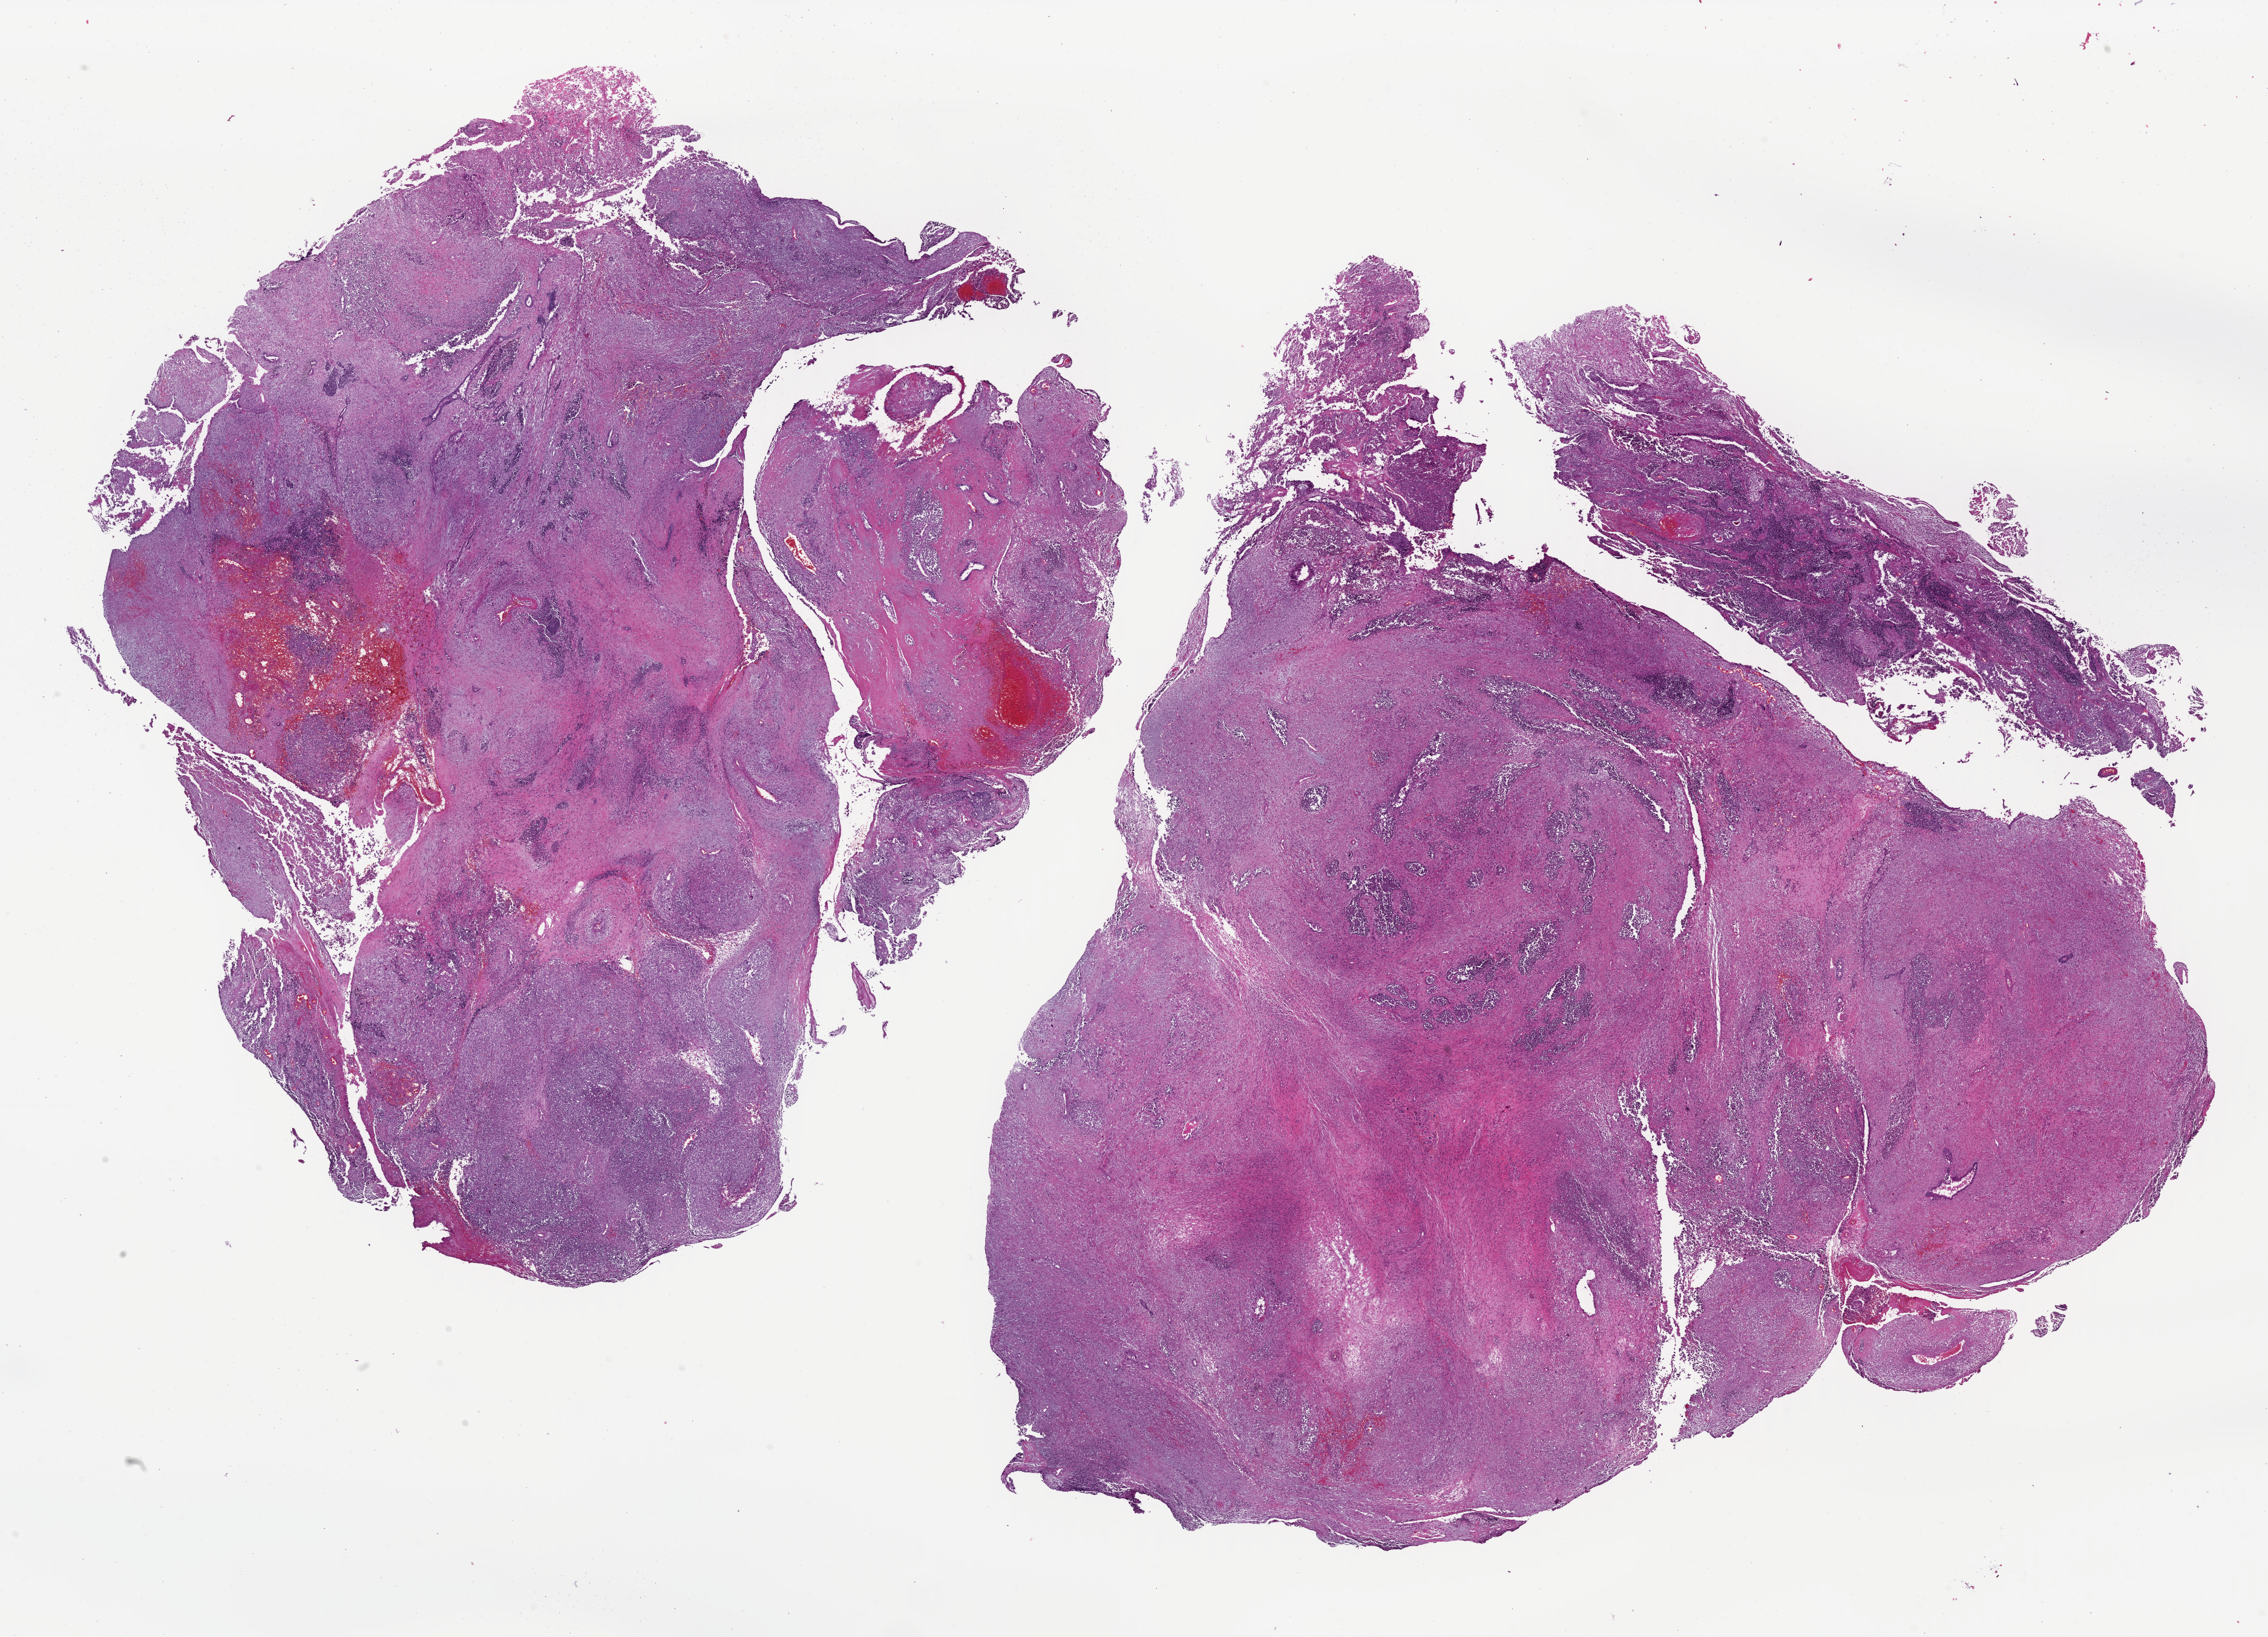
Hematoxylin and eosin (H&E) stained whole-slide image, low-resolution overview of the scanned area, about 29.5 x 21.3 mm (from a 40x scan); formalin-fixed paraffin-embedded (FFPE) diagnostic section; primary tumour sample from the uterus. Female patient; age at initial diagnosis 75 years.
* diagnosis: Carcinosarcoma, NOS
* FIGO stage: IIIC1